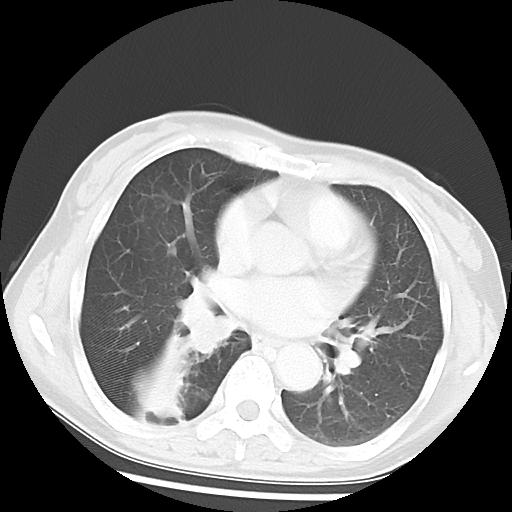
Chest CT, one axial slice; slice 28 of 52 in the series (ordered by position); reconstruction kernel LUNG; 120 kVp; lung window (W 1500 / L -600 HU); 512 × 512 image matrix, field of view 297 × 297 mm. Female patient, age 54 years. Case-level facts recorded for this patient, not image findings: clinical TNM (as recorded): T1c N0 M0; histopathological grade: G1-2.
Structures marked on this image (rectangle marked by the reading radiologist):
- lung tumour (recorded histology: squamous cell carcinoma): bounding box <164,283,228,368> (left, top, right, bottom; pixels)